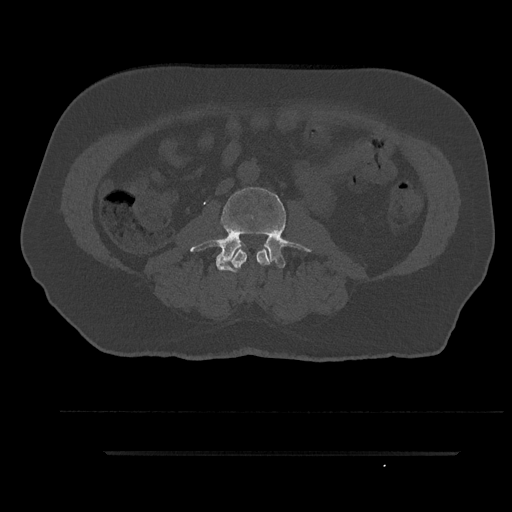
CT including the spine, one axial slice. 120 kVp. Bone window (W 1800 / L 400 HU). 512 × 512 image matrix. Patient: male, 63 years. From the clinical record (not read from this slice): primary cancer: renal.
Outlined on this slice (semi-automatically segmented with operator editing):
- L2 vertebra: bounding box <231,249,270,272> (left, top, right, bottom; pixels)
- L3 vertebra: <190,185,309,272>